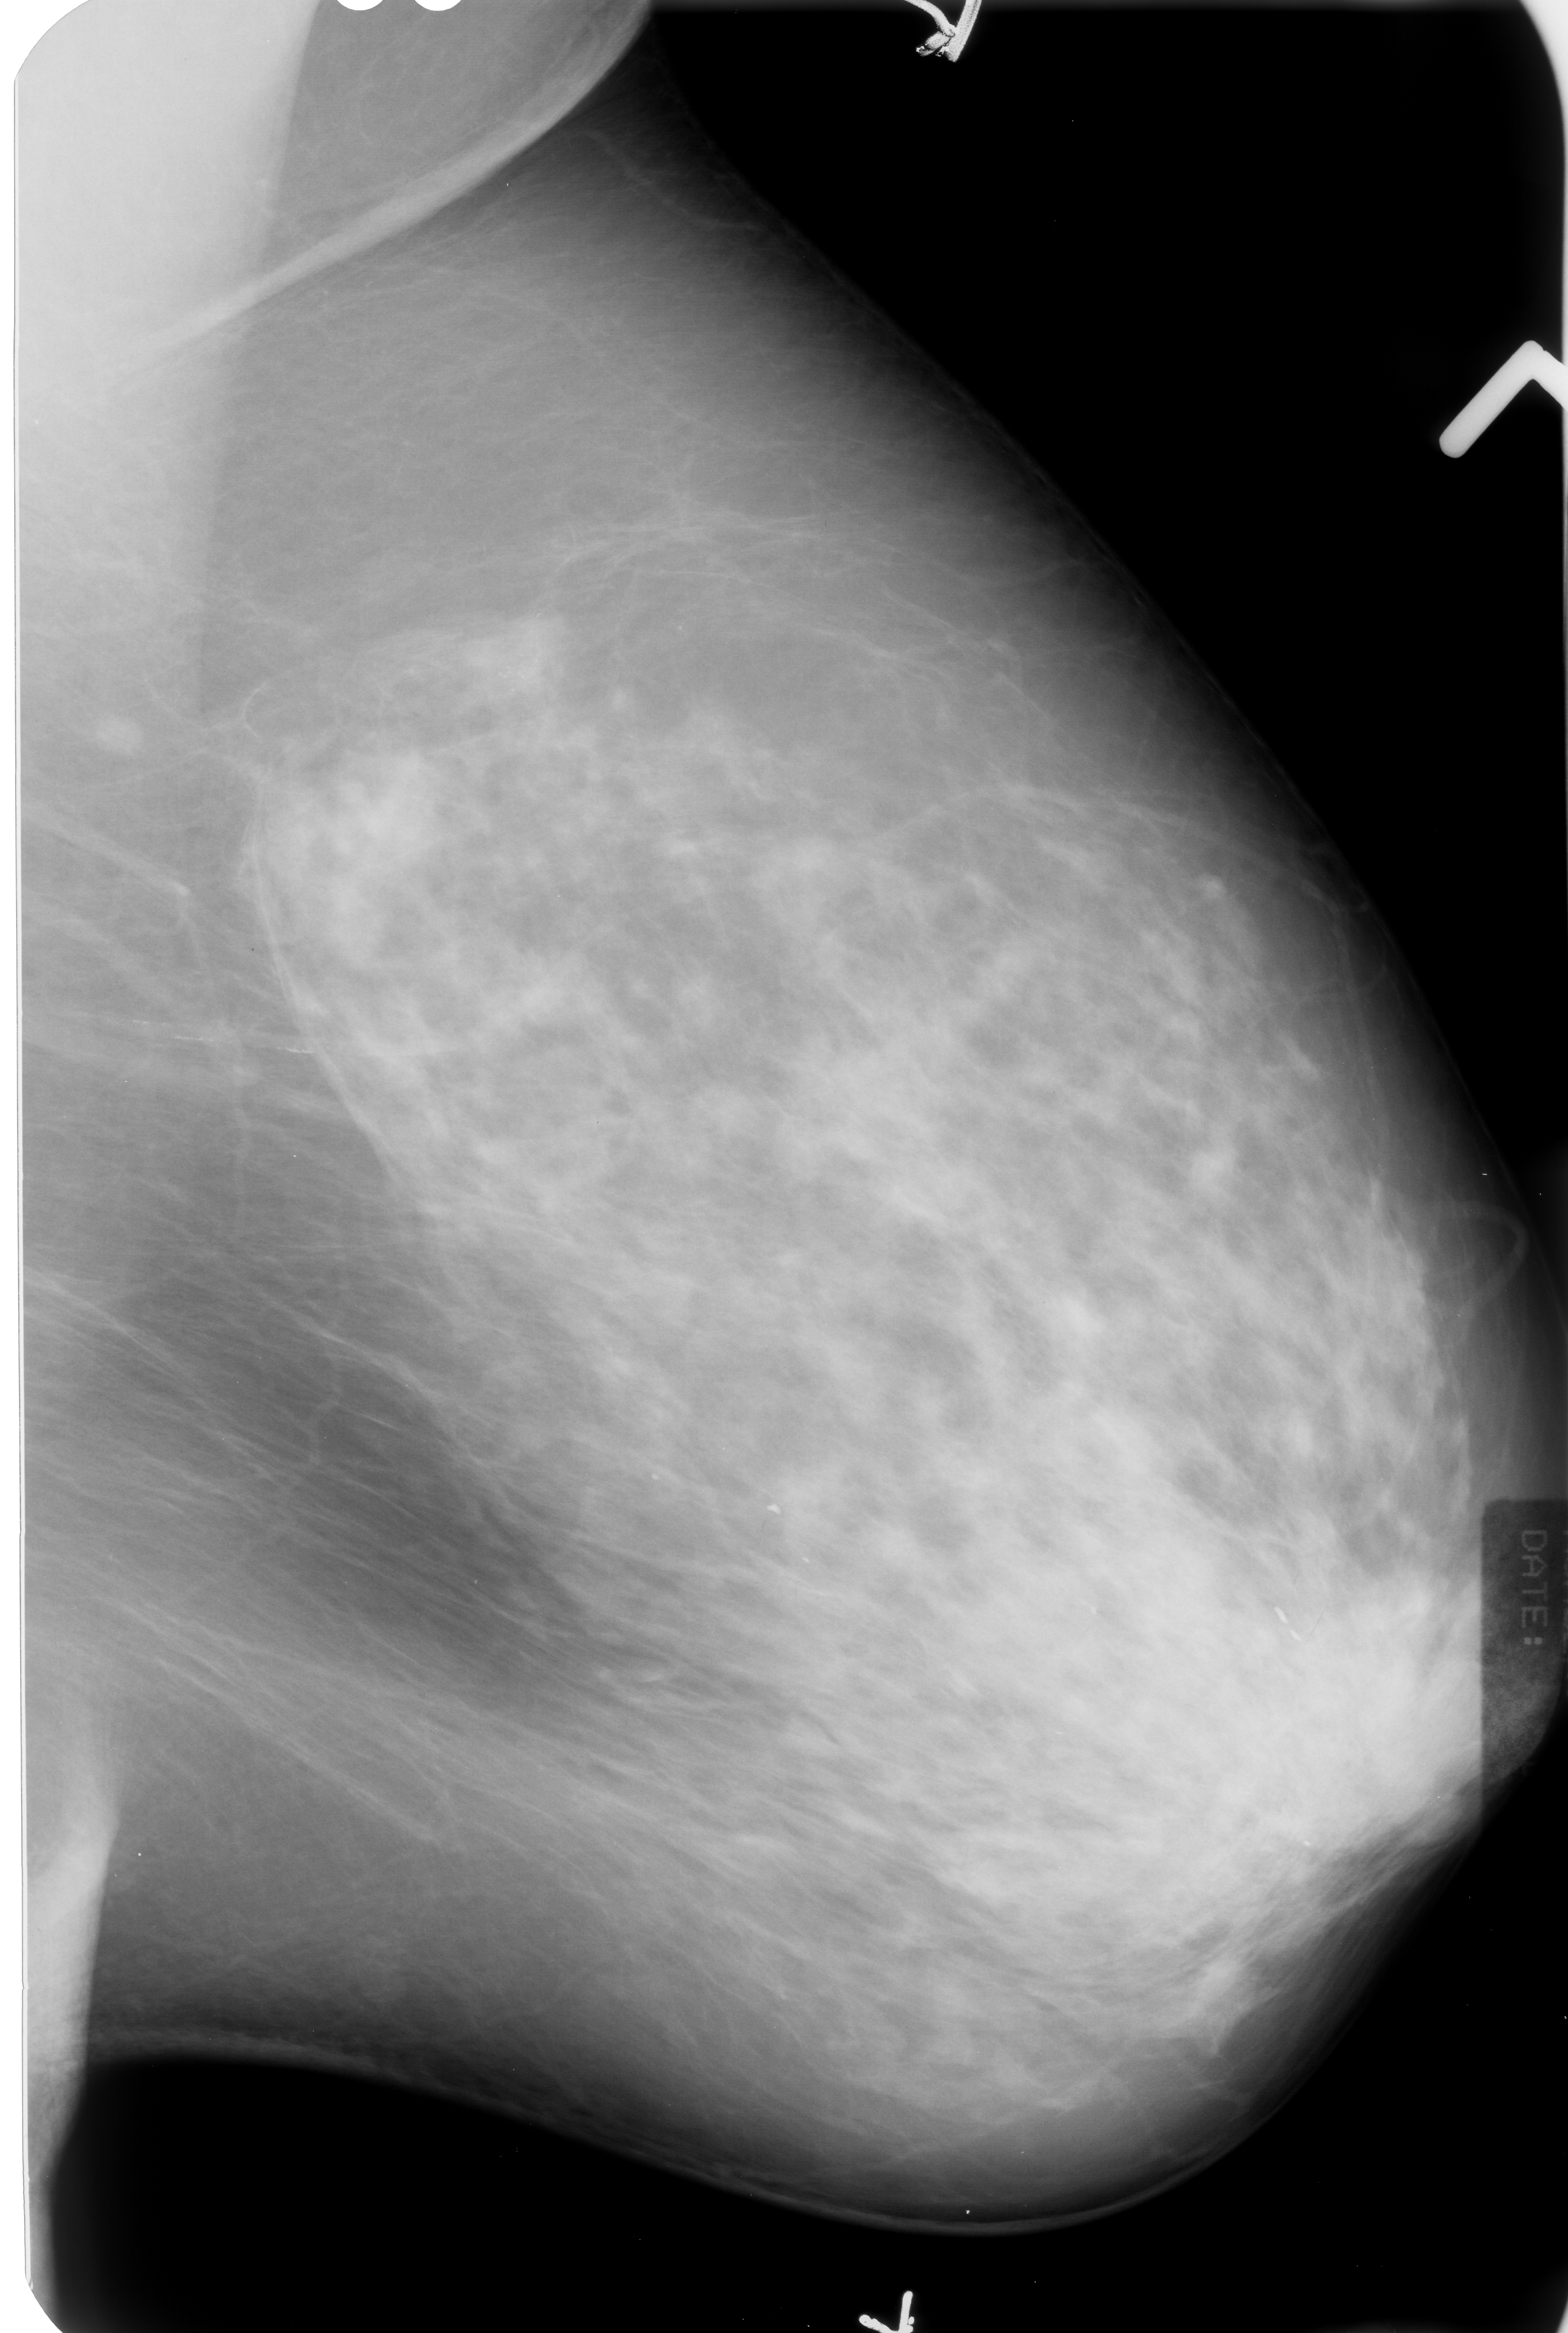
Scanned film-screen mammogram; left breast; MLO view; BI-RADS breast density category 3 (scale 1–4); 1568 × 2333 image matrix.
Expert-marked regions of interest on this image (one box per marked abnormality):
- Finding 1 of 3: calcifications, morphology vascular / coarse; BI-RADS assessment category 2; benign; no additional work-up was recommended (outcome (as recorded, no biopsy): benign without callback): bounding box <15,949,395,1077> (left, top, right, bottom; pixels)
- Finding 2 of 3: calcifications, morphology vascular / coarse; BI-RADS assessment category 2; outcome (as recorded, no biopsy): benign without callback (not worked up further): <724,1442,824,1566>
- Finding 3 of 3: calcifications, morphology vascular / coarse; BI-RADS assessment category 2; subtlety rating 3 on a 1 (subtle) to 5 (obvious) scale; benign; no additional work-up was recommended (outcome (as recorded, no biopsy): benign without callback): <1225,1544,1321,1636>